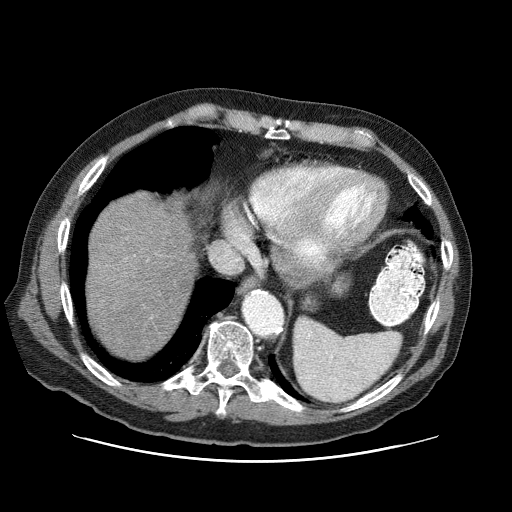
Contrast-enhanced abdominal CT (liver protocol), one axial slice. Position 67 of 87 along the scan axis. Reconstruction kernel STANDARD. 120 kVp. One of 3 acquisitions stored at this slice position. Soft-tissue window (W 400 / L 40 HU). 512 × 512 image matrix, field of view 400 × 400 mm. Case-level facts recorded for this patient, not image findings: diagnosis: hepatocellular carcinoma (patient treated with transarterial chemoembolisation; whether this scan precedes or follows treatment is not stated here); TNM stage (as recorded): Stage-IIIA; Child-Pugh class: A; tumour differentiation: well differentiated; tumour nodularity: multinodular.
Outlined on this slice (semi-automatic segmentation, software-assisted and operator-edited):
- liver parenchyma outside the tumour (the mass and vessels are separate outlines, so this box may not span the whole liver): bounding box [x1, y1, x2, y2] px = [86, 190, 196, 358]